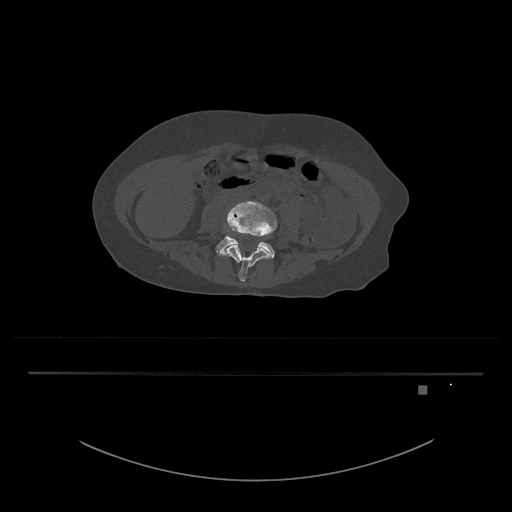
CT including the spine, one axial slice. Position 339 of 797 along the scan axis. Bone window (W 1800 / L 400 HU). 0.5 mm slice thickness. 512 × 512 image matrix. Patient: female, 57 years. Case-level facts recorded for this patient, not image findings: primary cancer: cervical.
Outlined on this slice (semi-automatic segmentation, software-assisted and operator-edited):
- L4 vertebra: bounding box (x1, y1, x2, y2) in pixels: (220, 201, 277, 282)